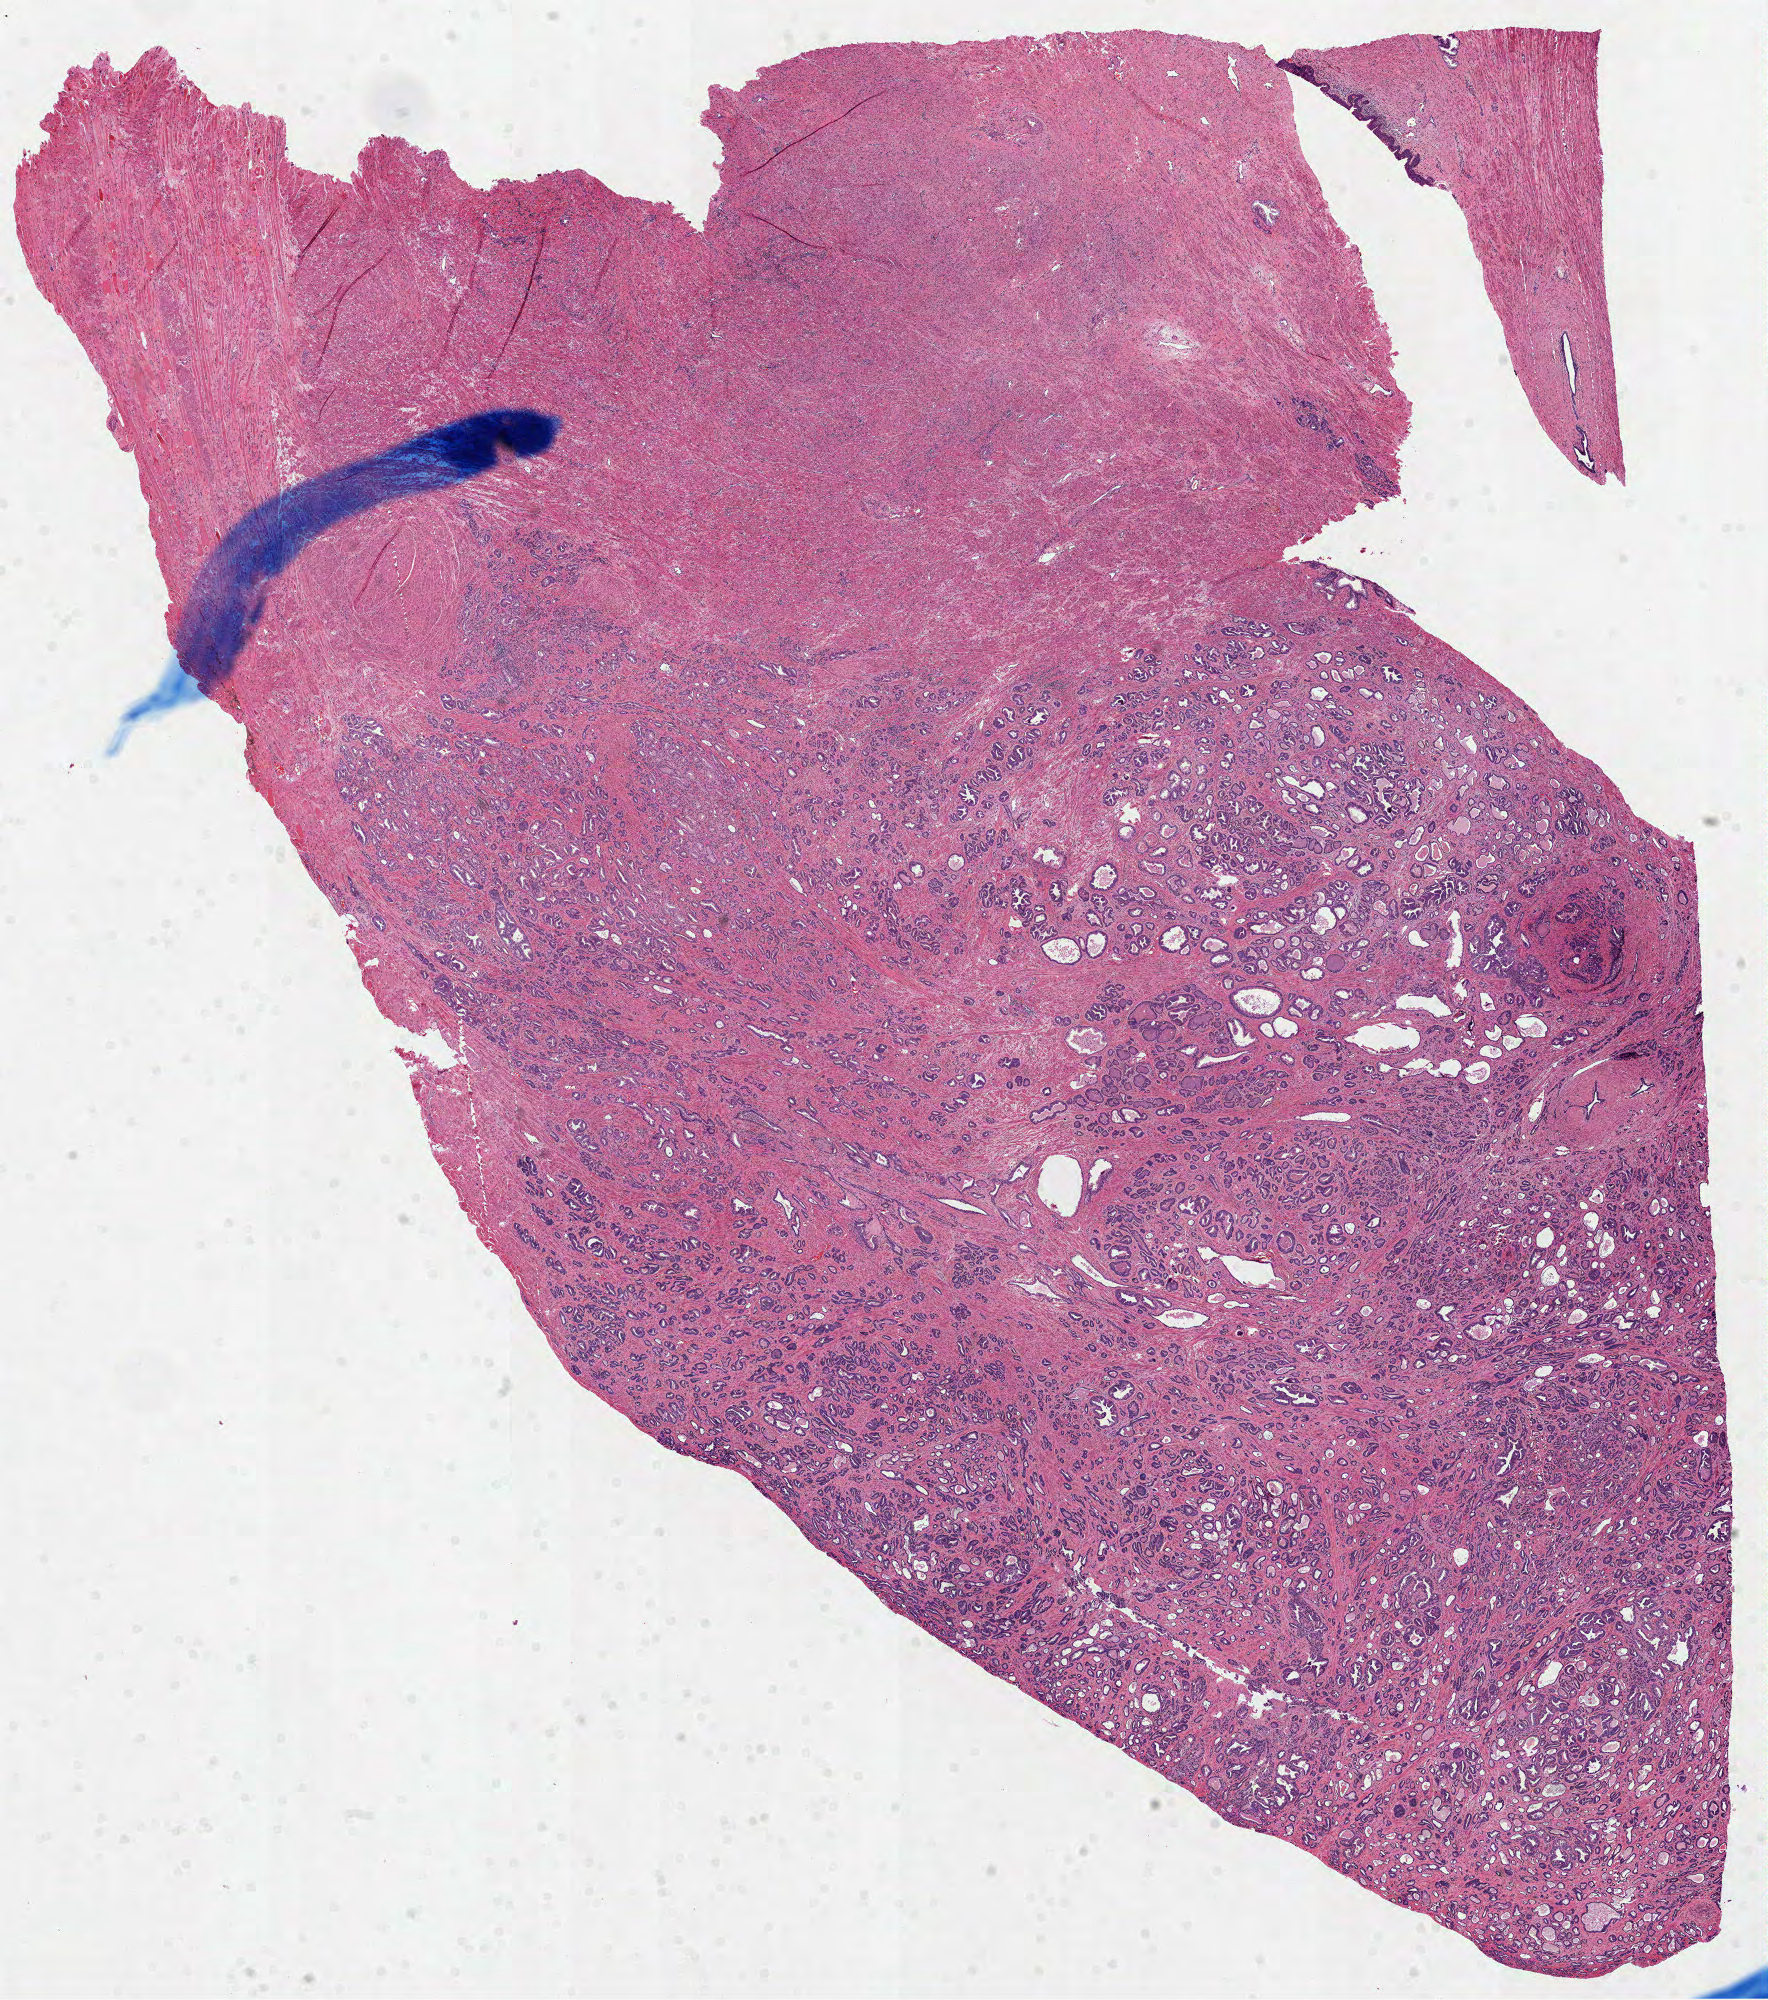
Digitized H&E-stained tissue section (whole slide), whole scanned area (about 14.3 x 16.1 mm, acquisition: 40x scan) shown as a low-resolution overview. FFPE section. Sample: primary tumour, prostate. Male patient; age at initial diagnosis 55 years. Gleason score: 7 (3+4).
Lymph nodes positive (case pathology): 0 of 15 examined. Laterality: bilateral. Diagnosis: Acinar cell carcinoma (prostate gland).